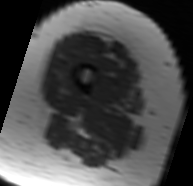
MRI of an extremity soft-tissue mass, one axial slice; slice 10 of 91 in the series (ordered by position); MR volume resampled by the dataset authors to the PET/CT grid (not the native acquisition matrix); 193 × 186 image matrix, field of view 188 × 182 mm. Female patient. Case-level facts recorded for this patient, not image findings: histological type: malignant solitary fibrous tumor; grade: intermediate; site of the primary tumour: right thigh.
Annotated regions visible in this slice (expert contour drawn on MRI and transferred to this co-registered scan by the dataset authors):
- gross tumour volume including surrounding oedema: bounding box [x1, y1, x2, y2] px = [83, 42, 123, 66]